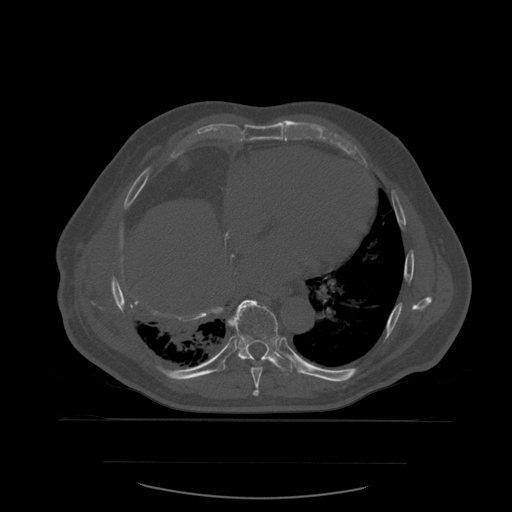
CT including the spine, one axial slice; position 349 of 590 along the scan axis; bone window (W 1800 / L 400 HU); 1.25 mm slice thickness; 512 × 512 image matrix, field of view 479 × 479 mm. Patient age 71 years. Case-level facts recorded for this patient, not image findings: primary cancer: lung; vertebrae with lytic lesions (as recorded): T1, T2, L5, S1.
Annotated regions visible in this slice (semi-automatic segmentation, software-assisted and operator-edited):
- T8 vertebra: bounding box (x1, y1, x2, y2) in pixels: (229, 321, 263, 396)
- T9 vertebra: (222, 300, 295, 376)